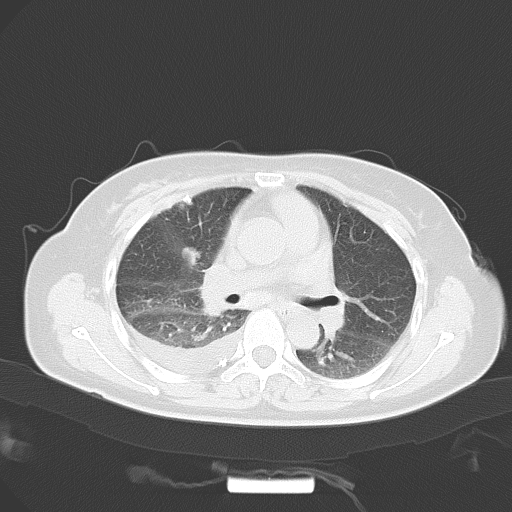
Chest CT, one axial slice; slice 21 of 41 in the series (ordered by position); reconstruction kernel B70f; 120 kVp; lung window (W 1500 / L -600 HU); 512 × 512 image matrix, field of view 360 × 360 mm. Patient: female, 53 years. From the clinical record (not read from this slice): clinical TNM (as recorded): T1c N1 M1b.
Annotated regions visible in this slice (bounding box drawn by a radiologist):
- lung tumour (recorded histology: adenocarcinoma): bounding box [x1, y1, x2, y2] px = [178, 243, 207, 274]